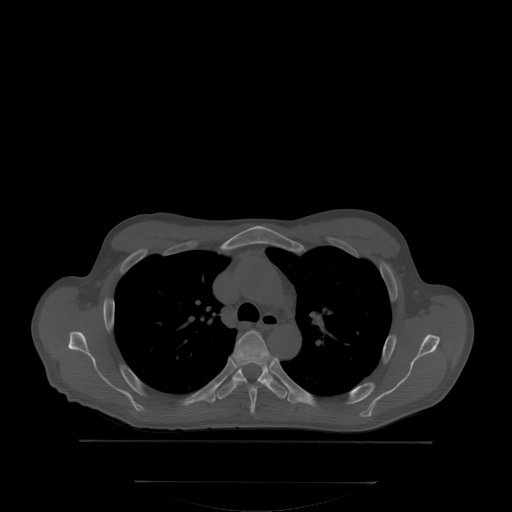
CT including the spine, one axial slice. Slice 253 of 350 in the series (ordered by position). Bone window (W 1800 / L 400 HU). 512 × 512 image matrix, field of view 500 × 500 mm. Male patient, age 58 years. From the clinical record (not read from this slice): primary cancer: prostate.
Structures marked on this image (semi-automatic segmentation, software-assisted and operator-edited):
- T4 vertebra: bounding box [x1, y1, x2, y2] px = [232, 331, 271, 412]
- T5 vertebra: [217, 362, 288, 398]